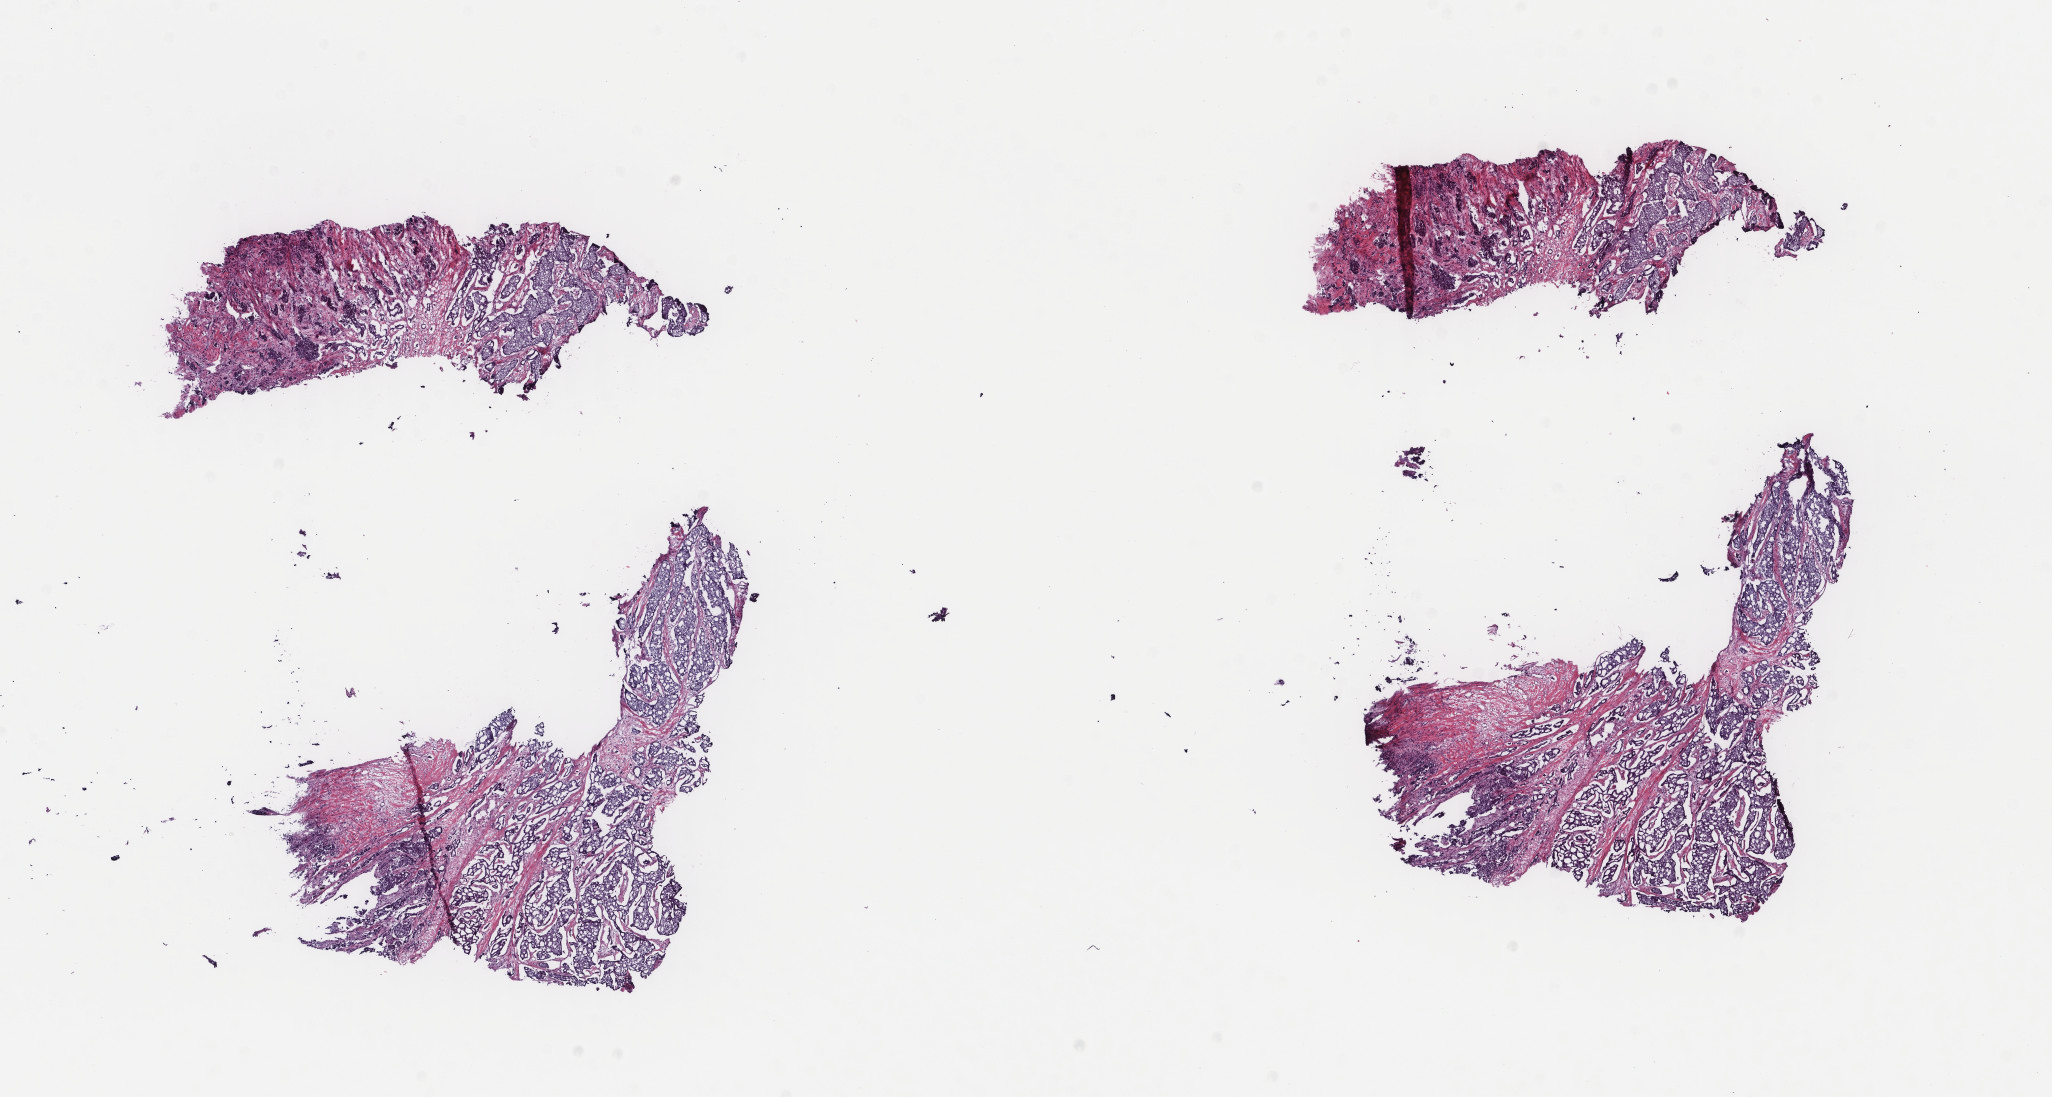
Whole-slide histology image, Hematoxylin and eosin (H&E) stained — whole scanned area (about 16.3 x 8.7 mm, acquisition: 40x scan) shown as a low-resolution overview, frozen section from the bottom of the tissue portion, sample: primary tumour, breast. Female patient; age at initial diagnosis 39 years. Slide review estimates, as recorded: tumour cells 80%, tumour nuclei 90%, normal cells 0%, stromal cells 19%, necrosis 1%. Infiltration values recorded for this section: lymphocyte infiltration 1%, monocyte infiltration 0%, neutrophil infiltration 0%.
• histologic diagnosis: Infiltrating duct carcinoma, NOS
• AJCC pathologic stage: IIA
• lymph nodes positive (case pathology): 0 of 5 examined